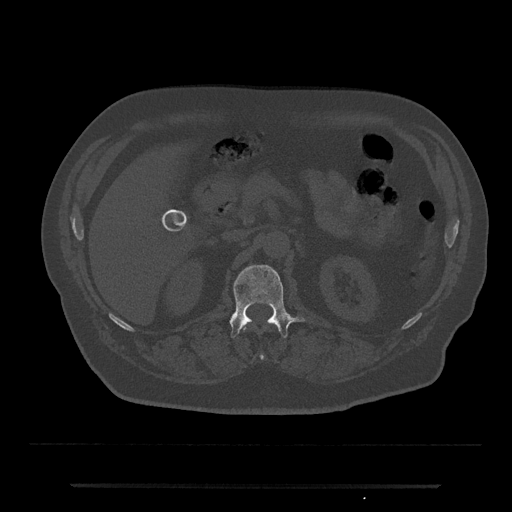
CT including the spine, one axial slice; position 548 of 797 along the scan axis; reconstruction kernel Br40s/3; bone window (W 1800 / L 400 HU); 0.5 mm slice thickness; 512 × 512 image matrix. Patient: male, 80 years. Case-level facts recorded for this patient, not image findings: primary cancer: prostate.
Annotated regions visible in this slice (semi-automatically segmented with operator editing):
- L1 vertebra: bounding box (x1, y1, x2, y2) in pixels: (229, 265, 305, 338)
- T12 vertebra: (242, 326, 263, 359)